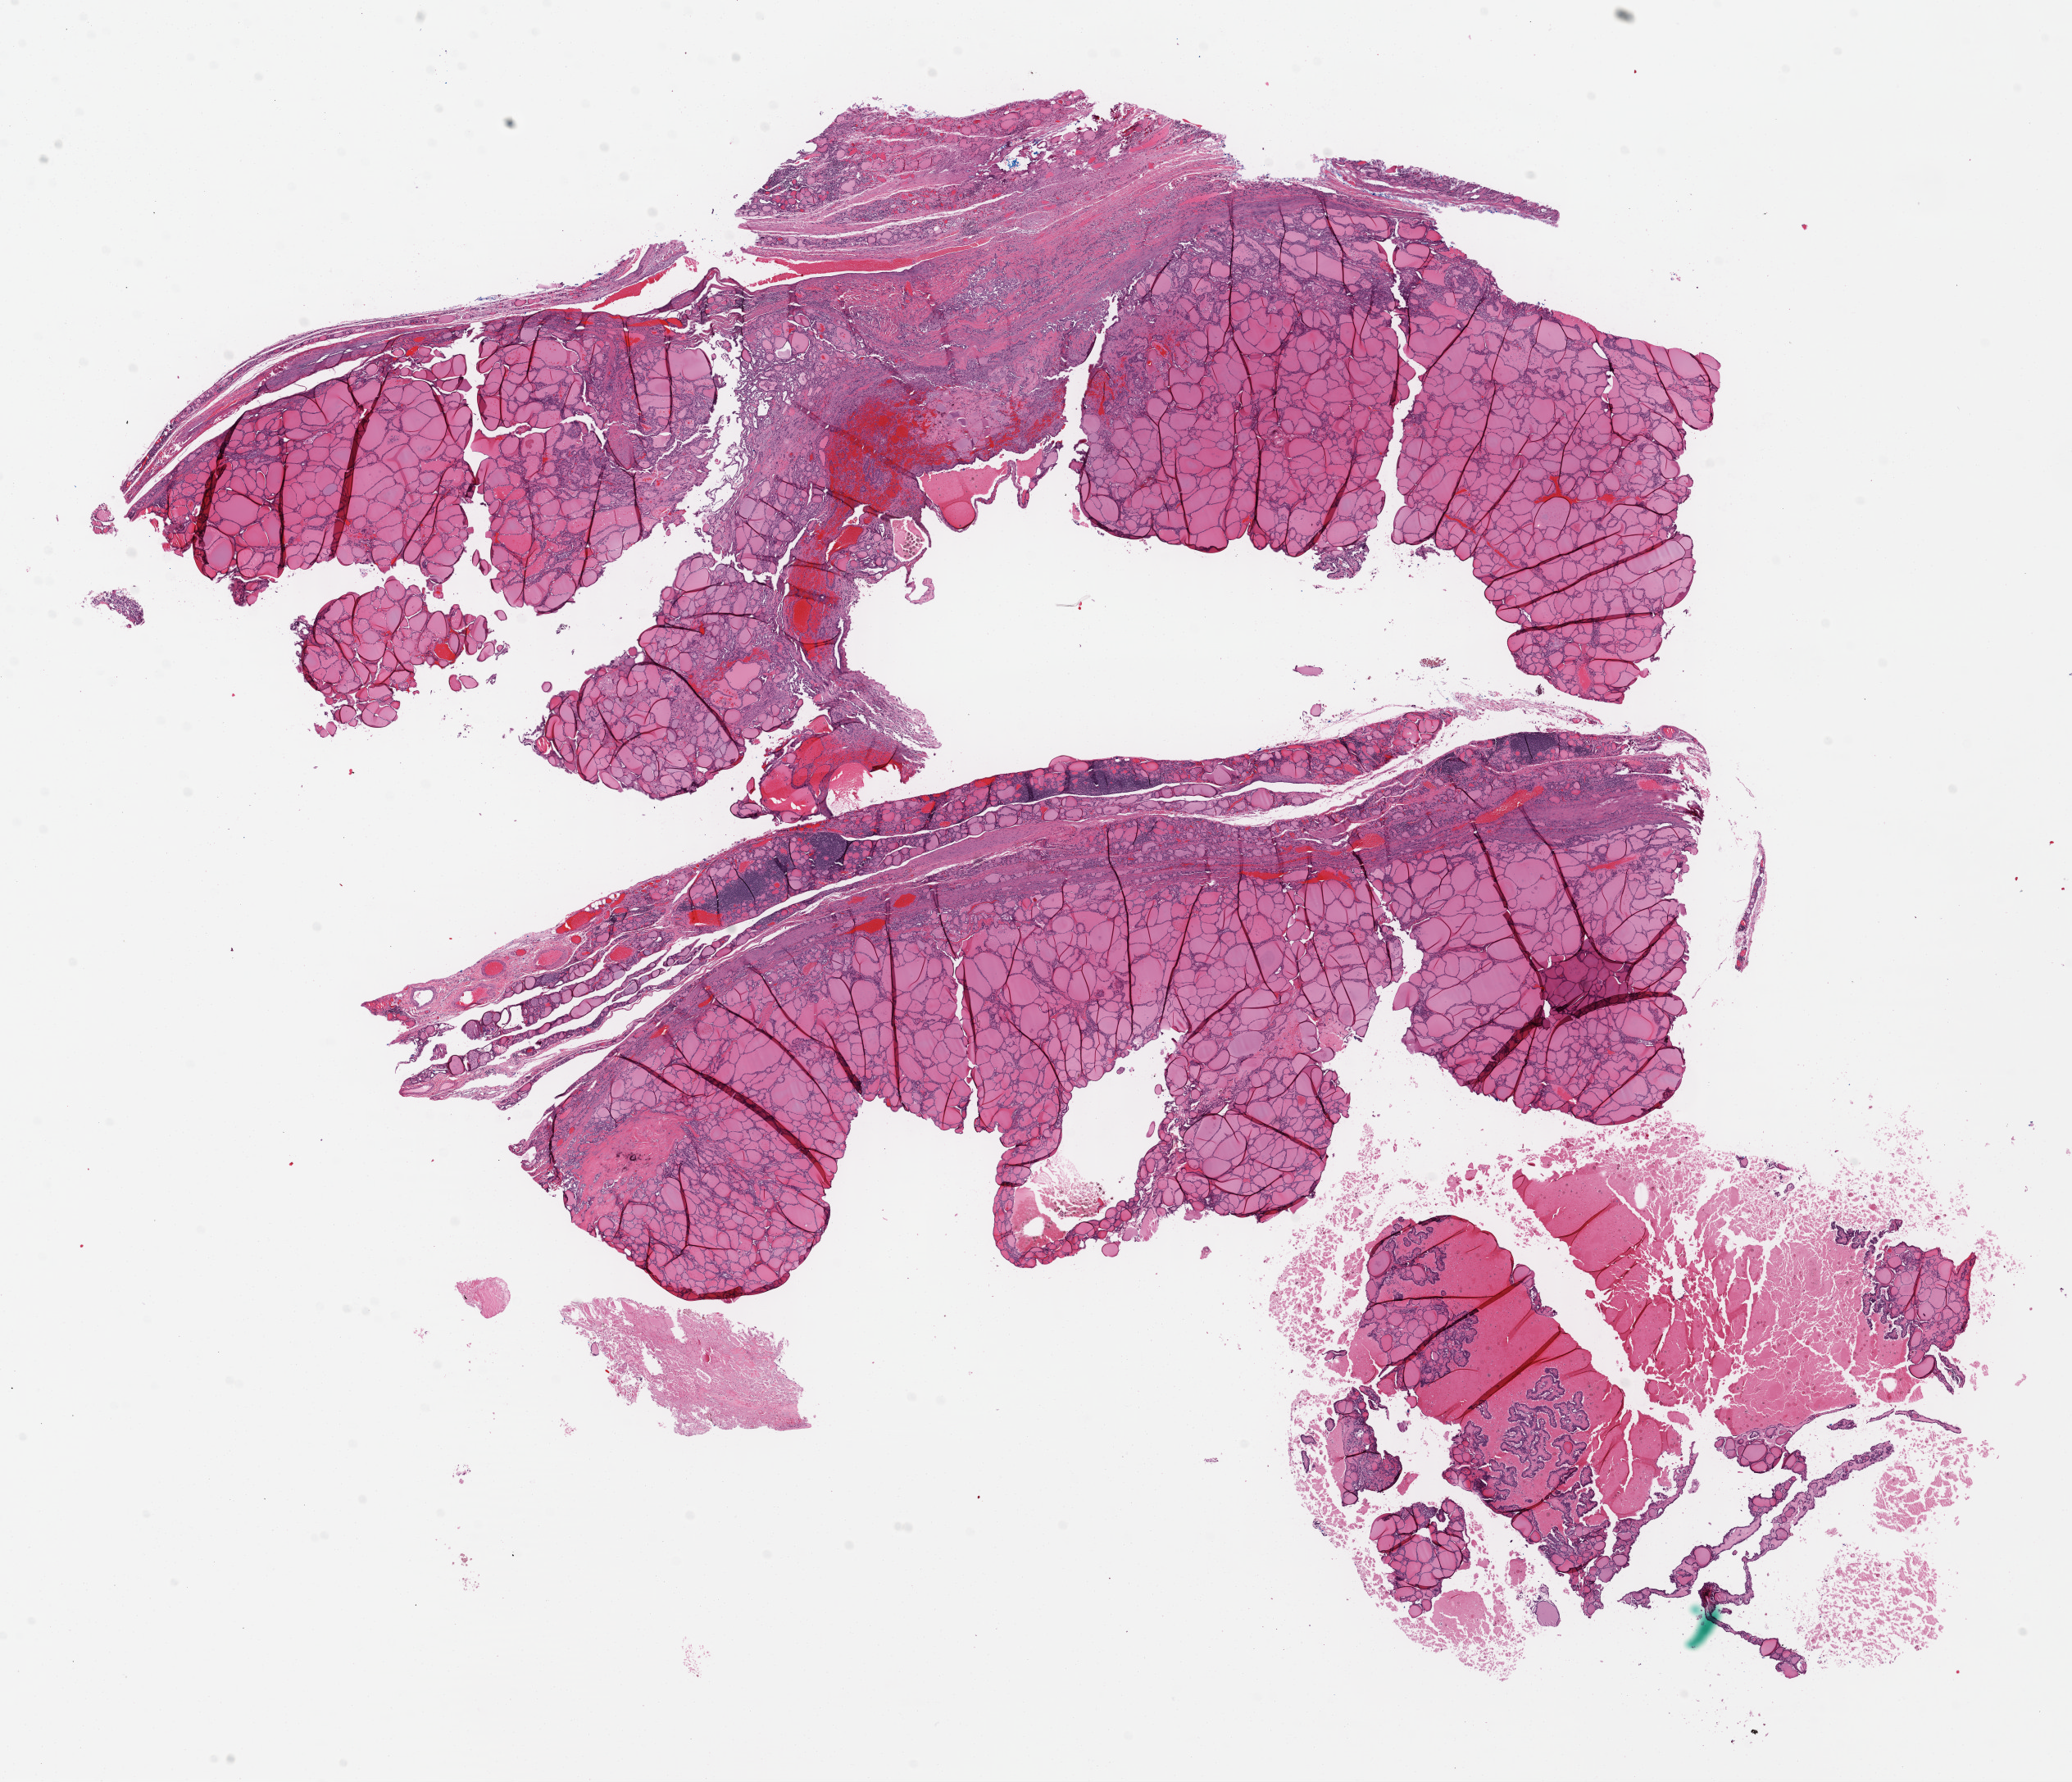
Hematoxylin and eosin (H&E) stained whole-slide image — low-resolution overview of the scanned area, about 19.9 x 17.1 mm, formalin-fixed paraffin-embedded (FFPE) diagnostic section, thyroid, primary tumour sample. Patient: female, age at initial diagnosis 53 years.
* lymph nodes positive (case pathology): 0 of 7 examined
* AJCC pathologic stage: II (7th edition)
* diagnosis: Papillary adenocarcinoma, NOS (thyroid gland)
* TNM: T2 N0 M0